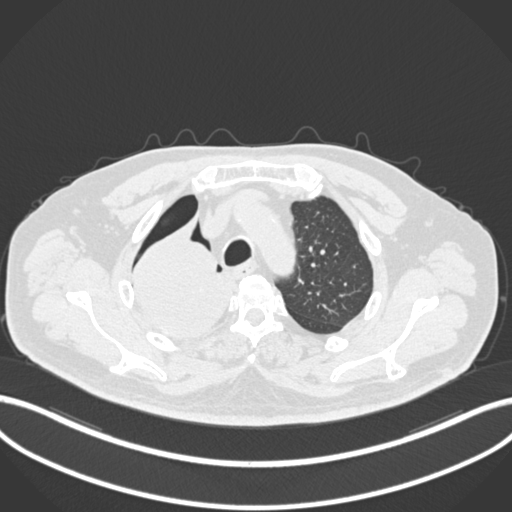
Chest CT, one axial slice; slice 168 of 218 in the series (ordered by position); reconstruction kernel B30f; 120 kVp; lung window (W 1500 / L -600 HU); 1 mm slice thickness; 512 × 512 image matrix. Male patient, age 68 years. Case-level facts recorded for this patient, not image findings: clinical TNM (as recorded): T2a N0 M0.
Annotated regions visible in this slice (rectangle marked by the reading radiologist):
- lung tumour (recorded histology: adenocarcinoma): bounding box (x1, y1, x2, y2) in pixels: (131, 223, 230, 343)